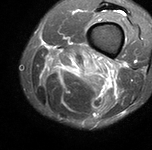
MRI of an extremity soft-tissue mass, one axial slice; slice 22 of 90 in the series (ordered by position); STIR; MR volume resampled by the dataset authors to the PET/CT grid (not the native acquisition matrix); 3.27 mm slice thickness; 152 × 150 image matrix, field of view 148 × 146 mm. Male patient. From the clinical record (not read from this slice): histological type: undifferentiated pleomorphic liposarcoma; grade: high; site of the primary tumour: left thigh.
Outlined on this slice (expert contour drawn on MRI and transferred to this co-registered scan by the dataset authors):
- gross tumour volume including surrounding oedema: bounding box [x1, y1, x2, y2] px = [41, 48, 119, 88]